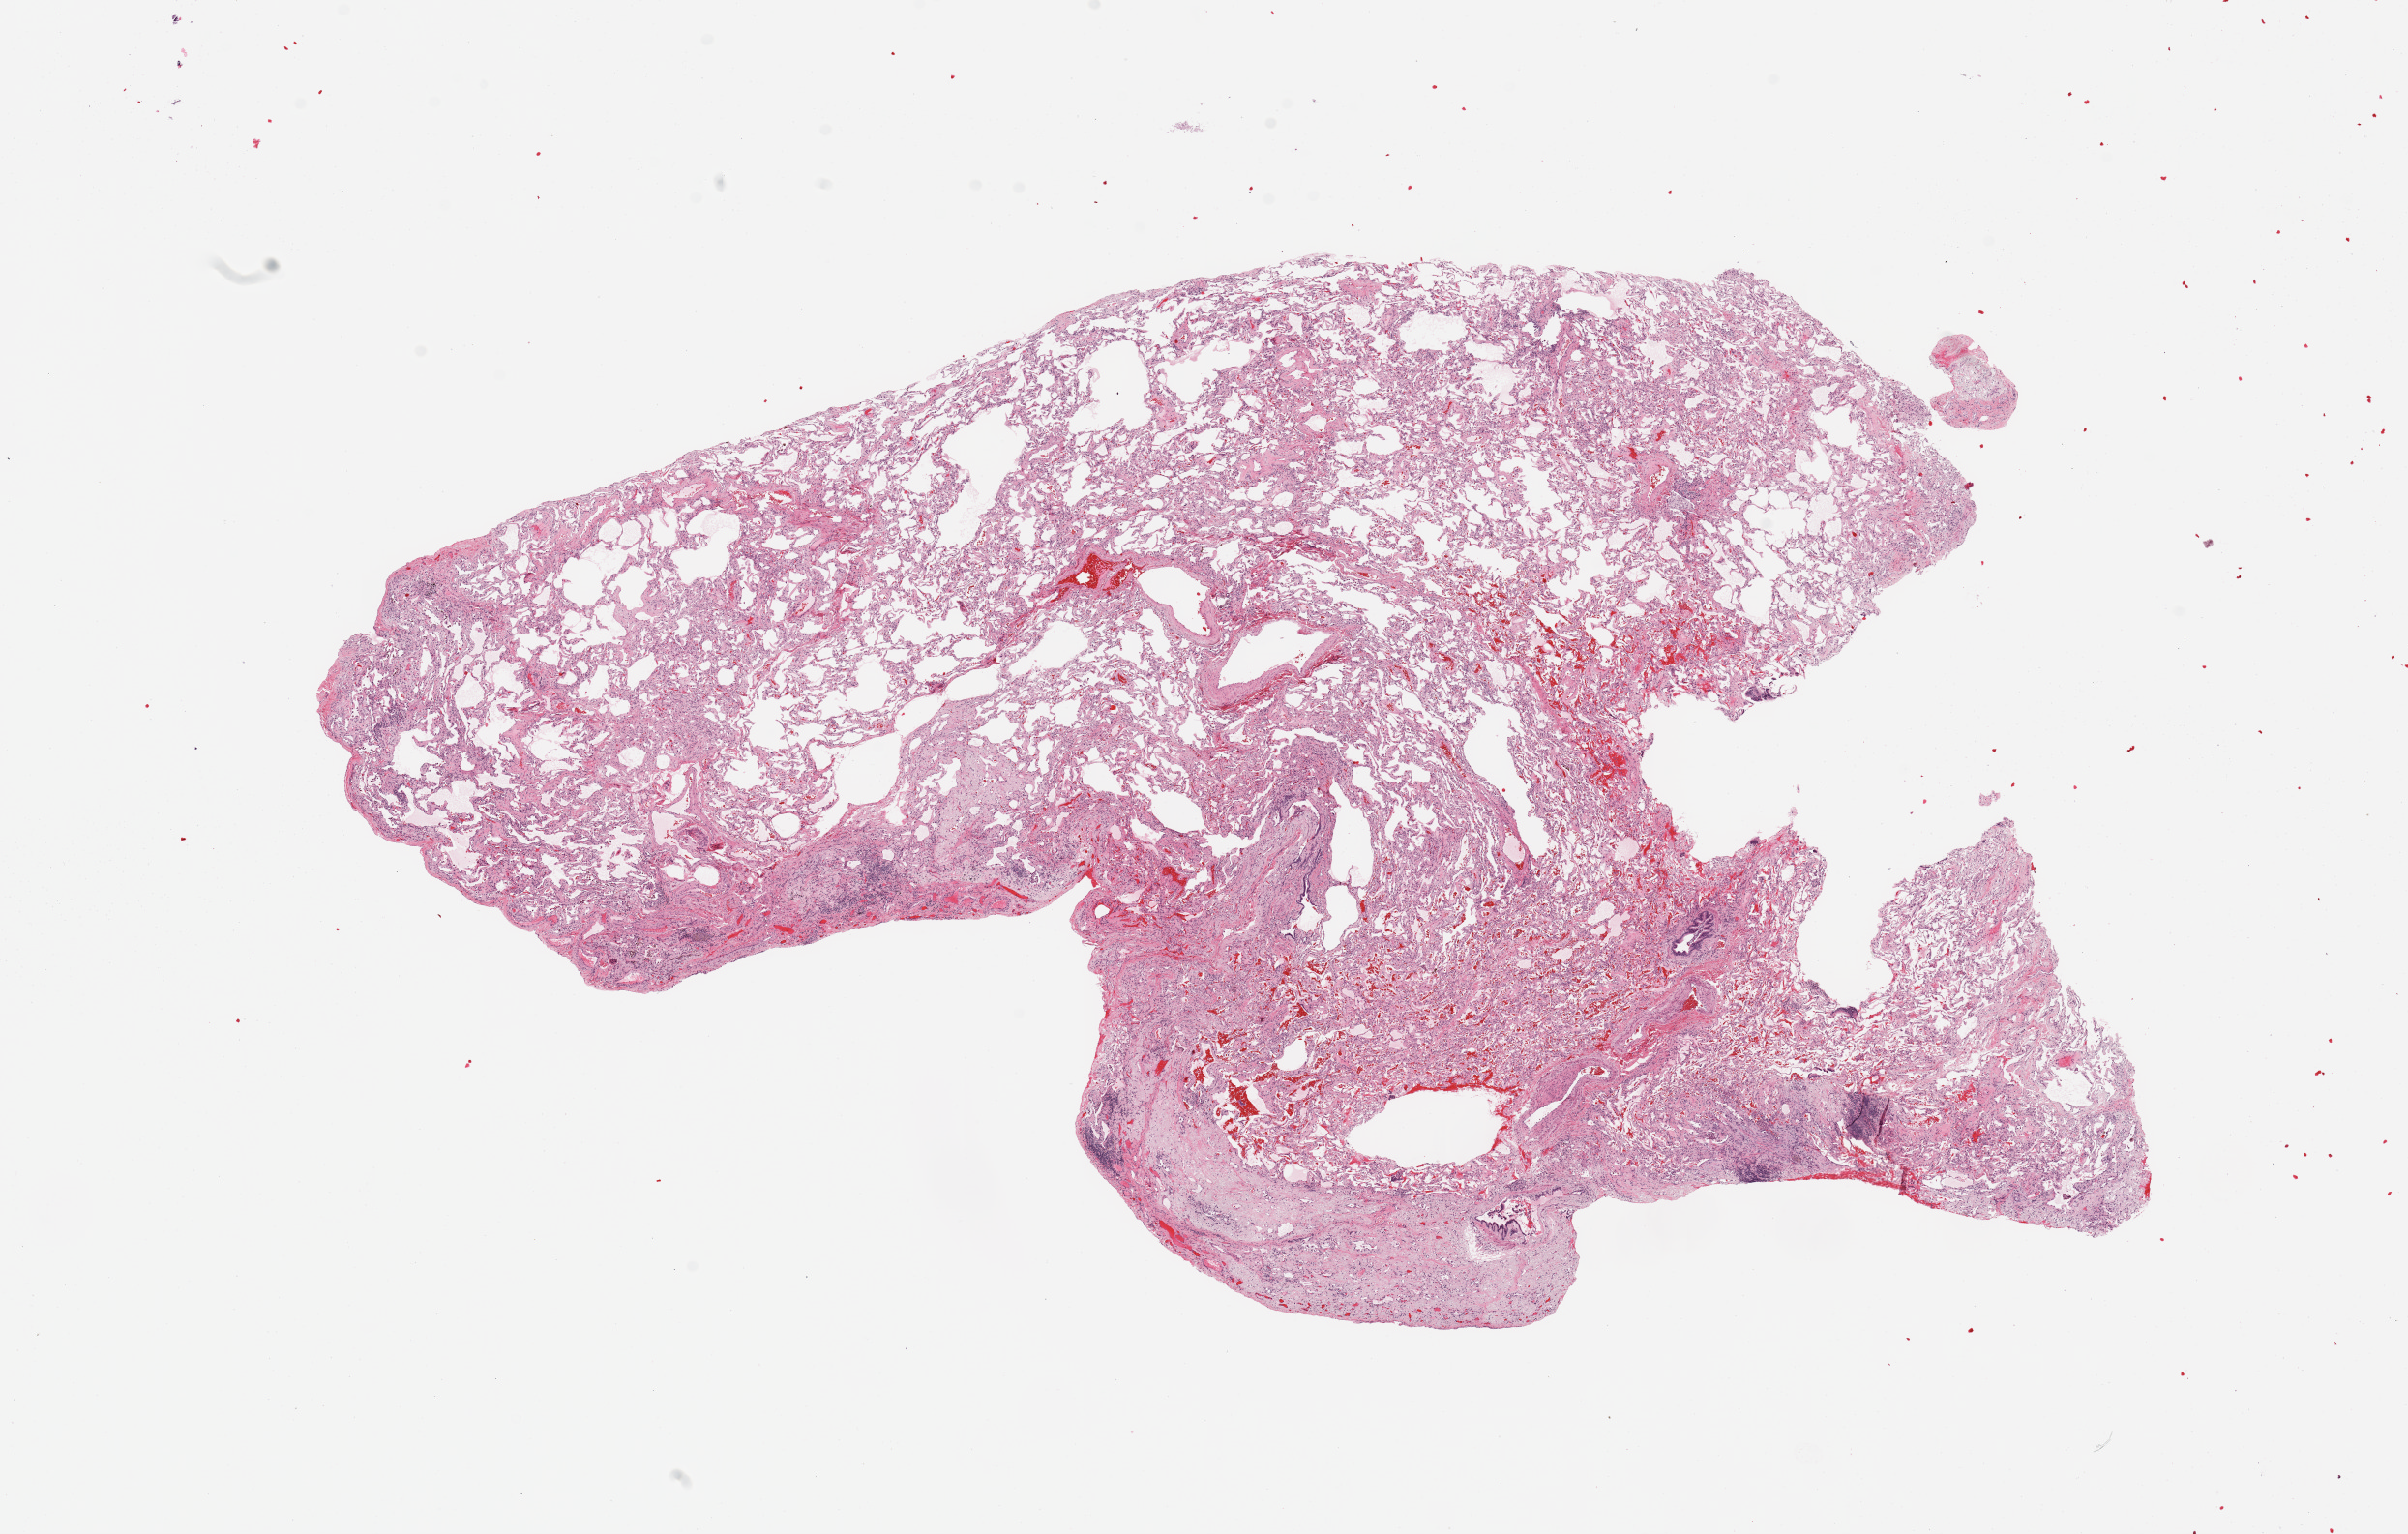
Whole-slide histology image, H&E-stained — low-resolution overview of the scanned area, about 19.7 x 12.5 mm (from a 20x scan); normal (non-tumour) tissue sample, sampled site: lung. 61-year-old female patient.
This section: normal (non-tumour) tissue from the same patient. Patient diagnosis: Adenocarcinoma, NOS.